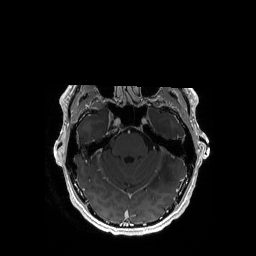
Brain MRI from a brain-tumour surgery series, one axial slice; slice 122 of 192 in the series (ordered by position); T1-weighted post-contrast; 256 × 256 image matrix, field of view 256 × 256 mm. From the clinical record (not read from this slice): histopathology: Astrocytoma; WHO grade: 3; IDH mutation: yes; tumour location: Left Temporal.
Annotated regions visible in this slice (outlined manually by an expert reader):
- tumour: bounding box (x1, y1, x2, y2) in pixels: (152, 124, 178, 186)